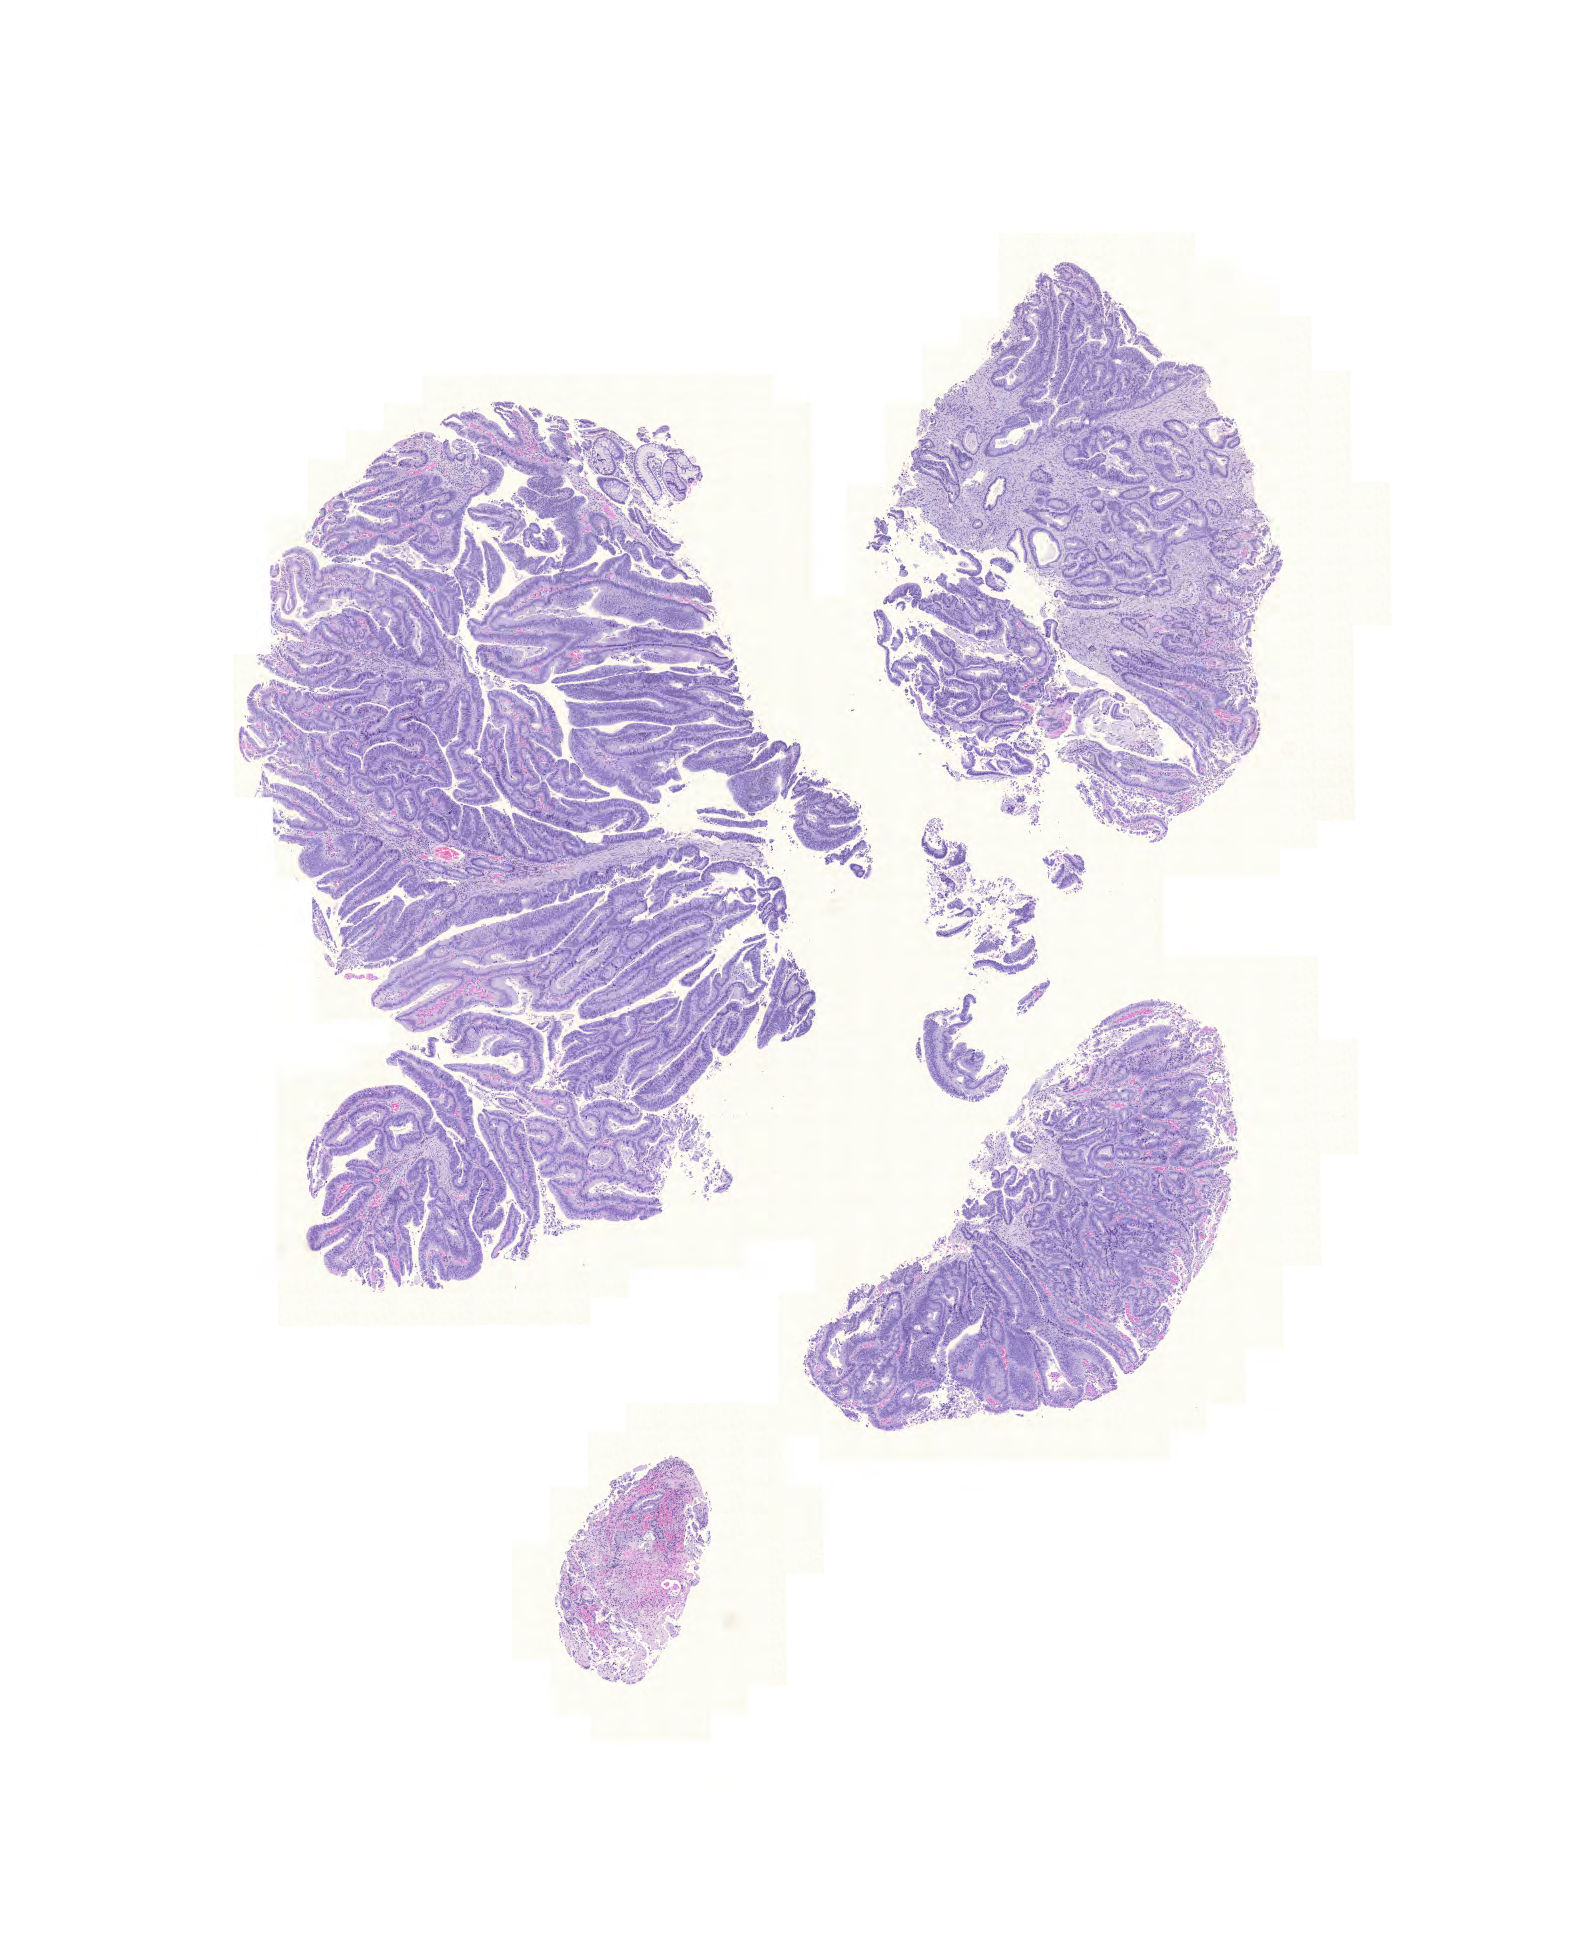
Digitized H&E tissue section (whole slide), a low-resolution overview of the entire scanned area, about 11.8 x 14.5 mm, formalin-fixed paraffin-embedded (FFPE) diagnostic section, sample: primary tumour, colon. Female, age 78 years at initial diagnosis.
Lymph nodes positive (case pathology): 7 of 18 examined. Histologic diagnosis: Adenocarcinoma, NOS. AJCC pathologic stage: IIIC (6th edition).